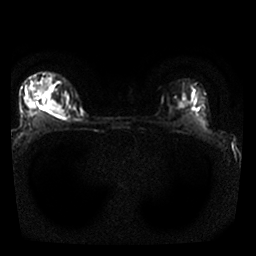
Breast MRI, one axial slice. Position 22 of 25 along the scan axis. Diffusion-weighted series; image 2 of 4 stored at this slice position (different b-values; order by instance number). 1.5 T. 4 mm slice thickness. 256 × 256 image matrix, field of view 310 × 310 mm. Female patient.
Structures marked on this image (outlined manually by an expert reader):
- tumour on diffusion-weighted imaging: box from (x=44, y=100) to (x=62, y=115) px